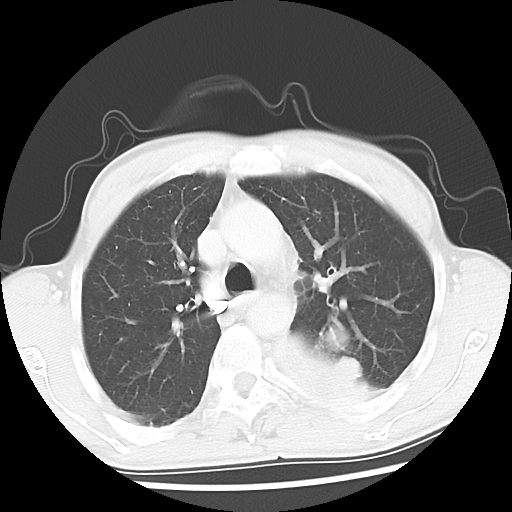
Chest CT, one axial slice; slice 36 of 52 in the series (ordered by position); reconstruction kernel LUNG; 120 kVp; lung window (W 1500 / L -600 HU); 5 mm slice thickness; 512 × 512 image matrix. Male patient, age 60 years. From the clinical record (not read from this slice): clinical TNM (as recorded): T4 N0 M0.
Annotated regions visible in this slice (bounding box drawn by a radiologist):
- lung tumour (recorded histology: squamous cell carcinoma): bounding box (x1, y1, x2, y2) in pixels: (266, 318, 419, 436)